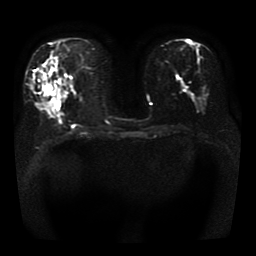
Breast MRI, one axial slice; slice 17 of 41 in the series (ordered by position); diffusion-weighted series; image 2 of 4 stored at this slice position (different b-values; order by instance number); 1.5 T; 256 × 256 image matrix, field of view 330 × 330 mm. Female patient.
Structures marked on this image (expert manual segmentation):
- tumour on diffusion-weighted imaging: bounding box (x1, y1, x2, y2) in pixels: (42, 82, 56, 99)